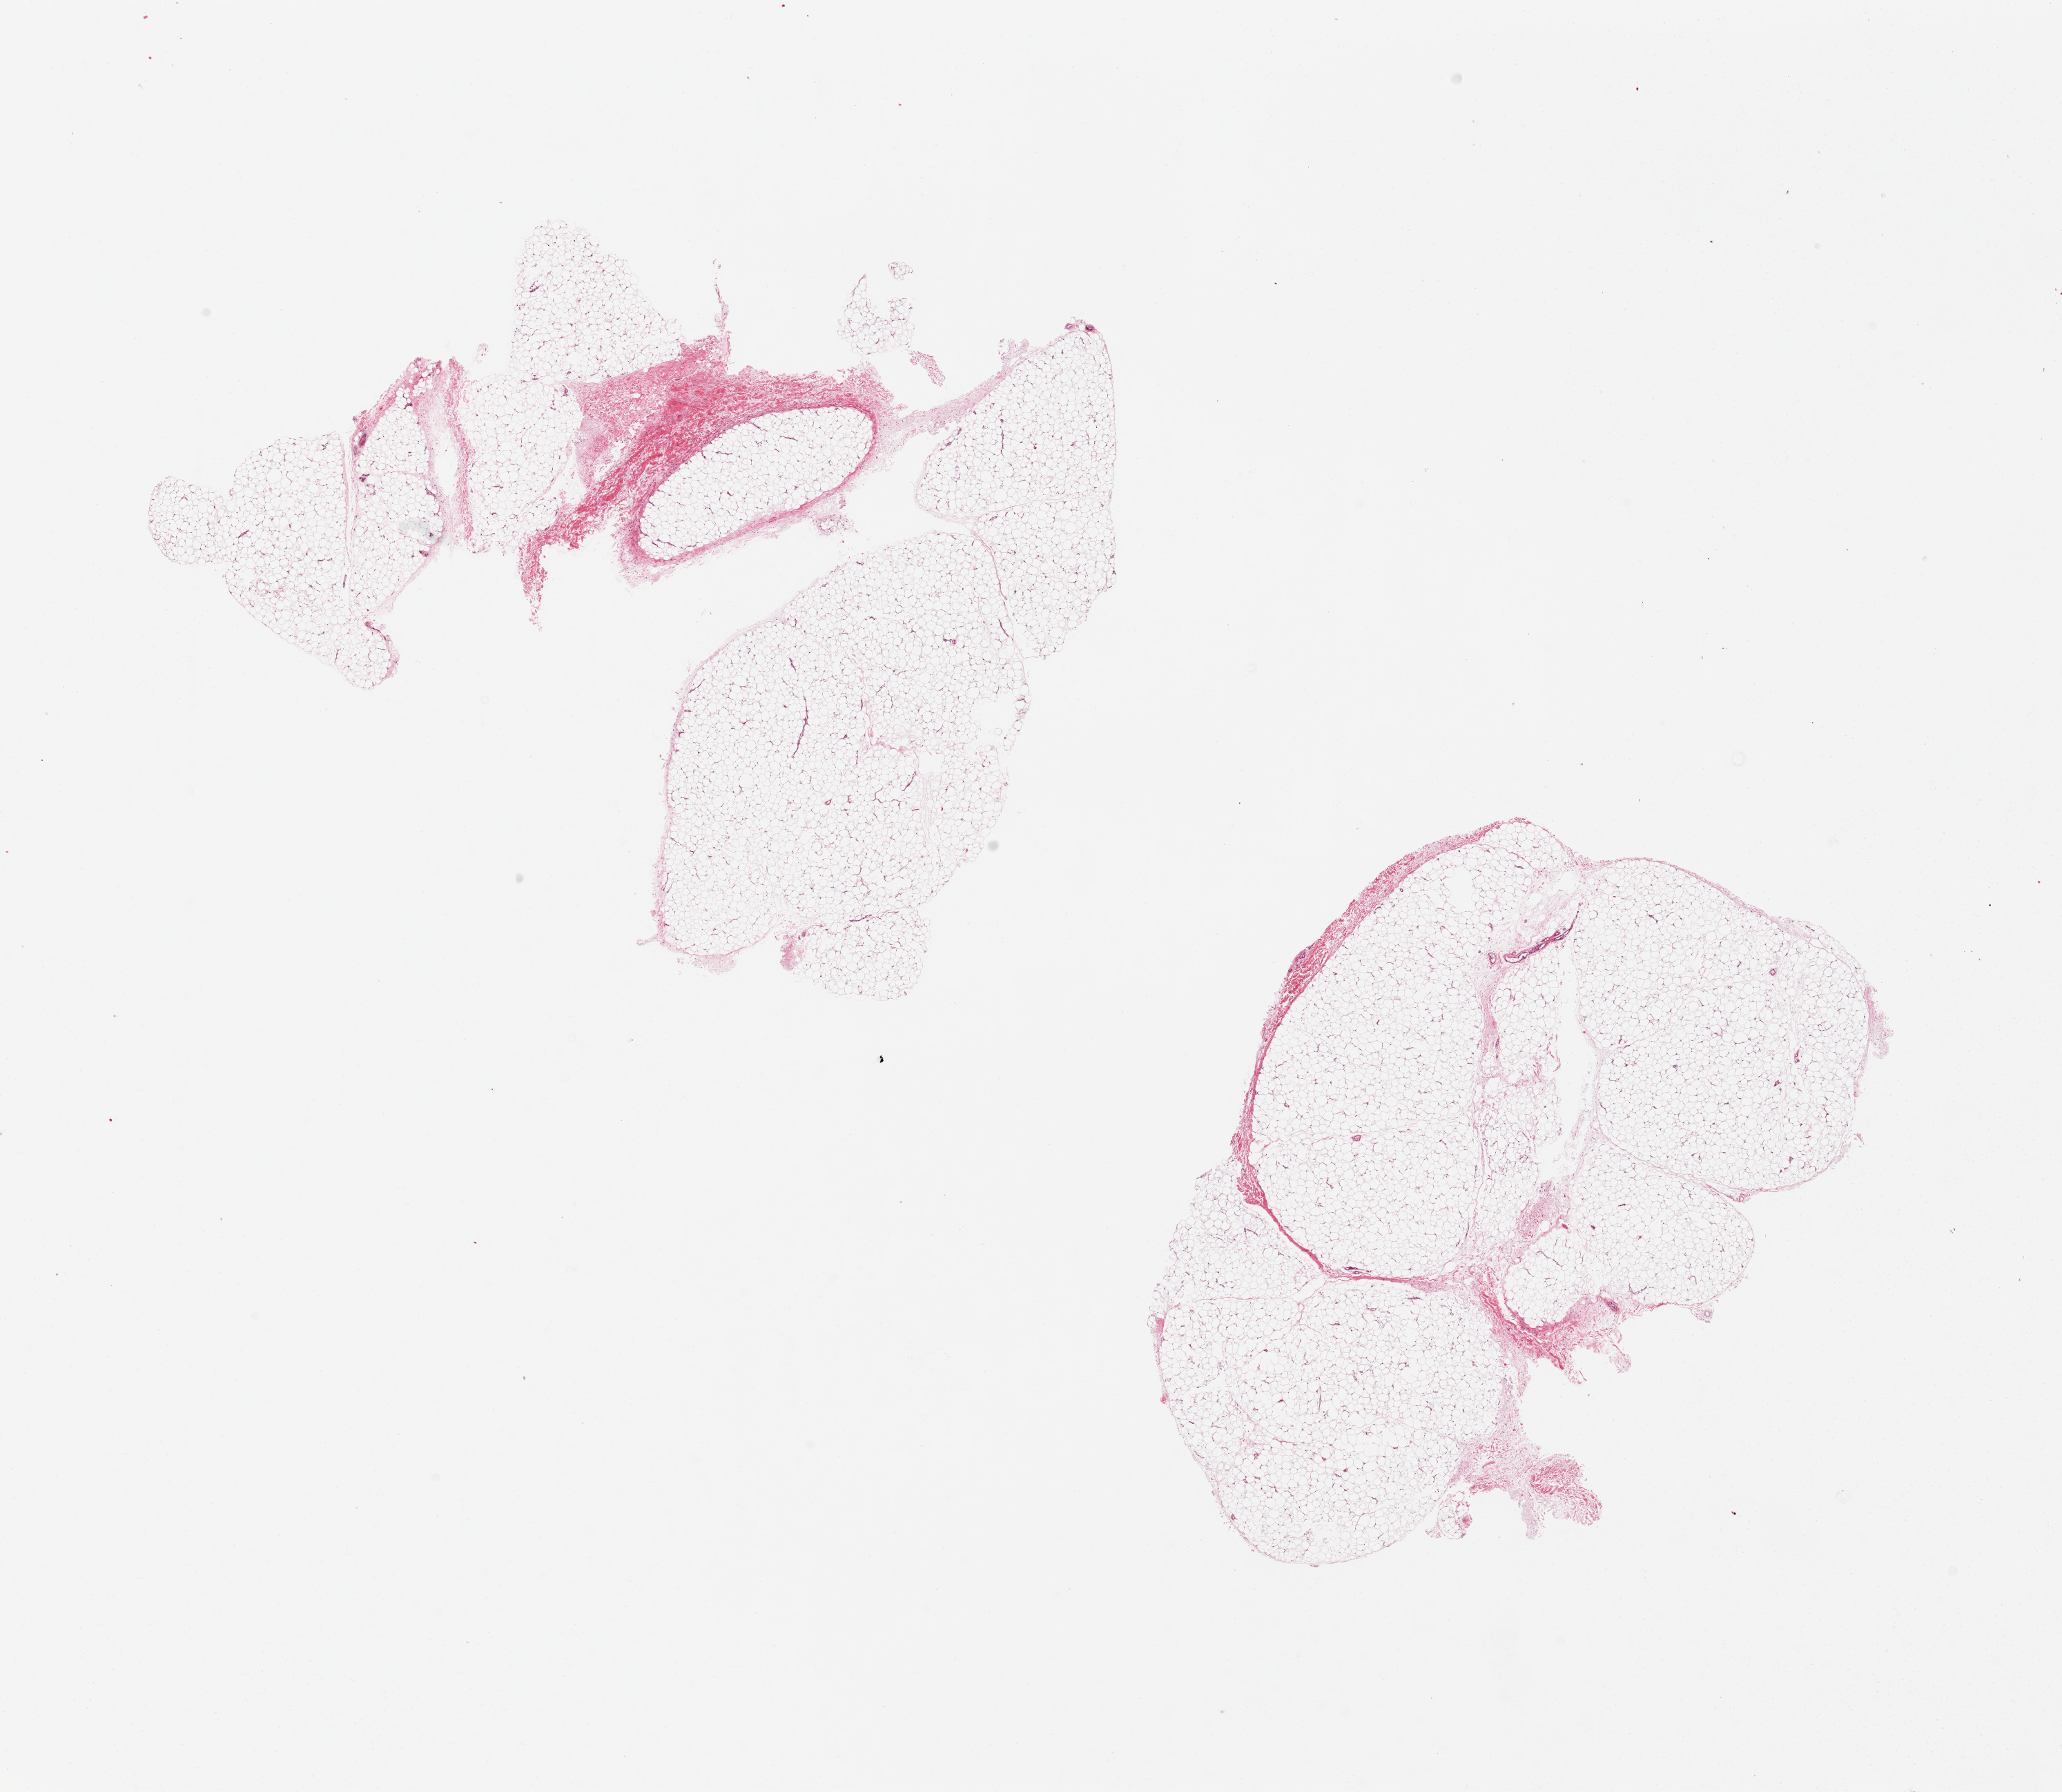
Hematoxylin and eosin (H&E) whole-slide image, a low-resolution overview of the entire scanned area, about 23.6 x 20.5 mm. PAXgene-fixed paraffin-embedded (PFPE) section. Section of adipose tissue (target tissue). Donor tissue sample.
* pathologist's review note for this sample: 2 pieces